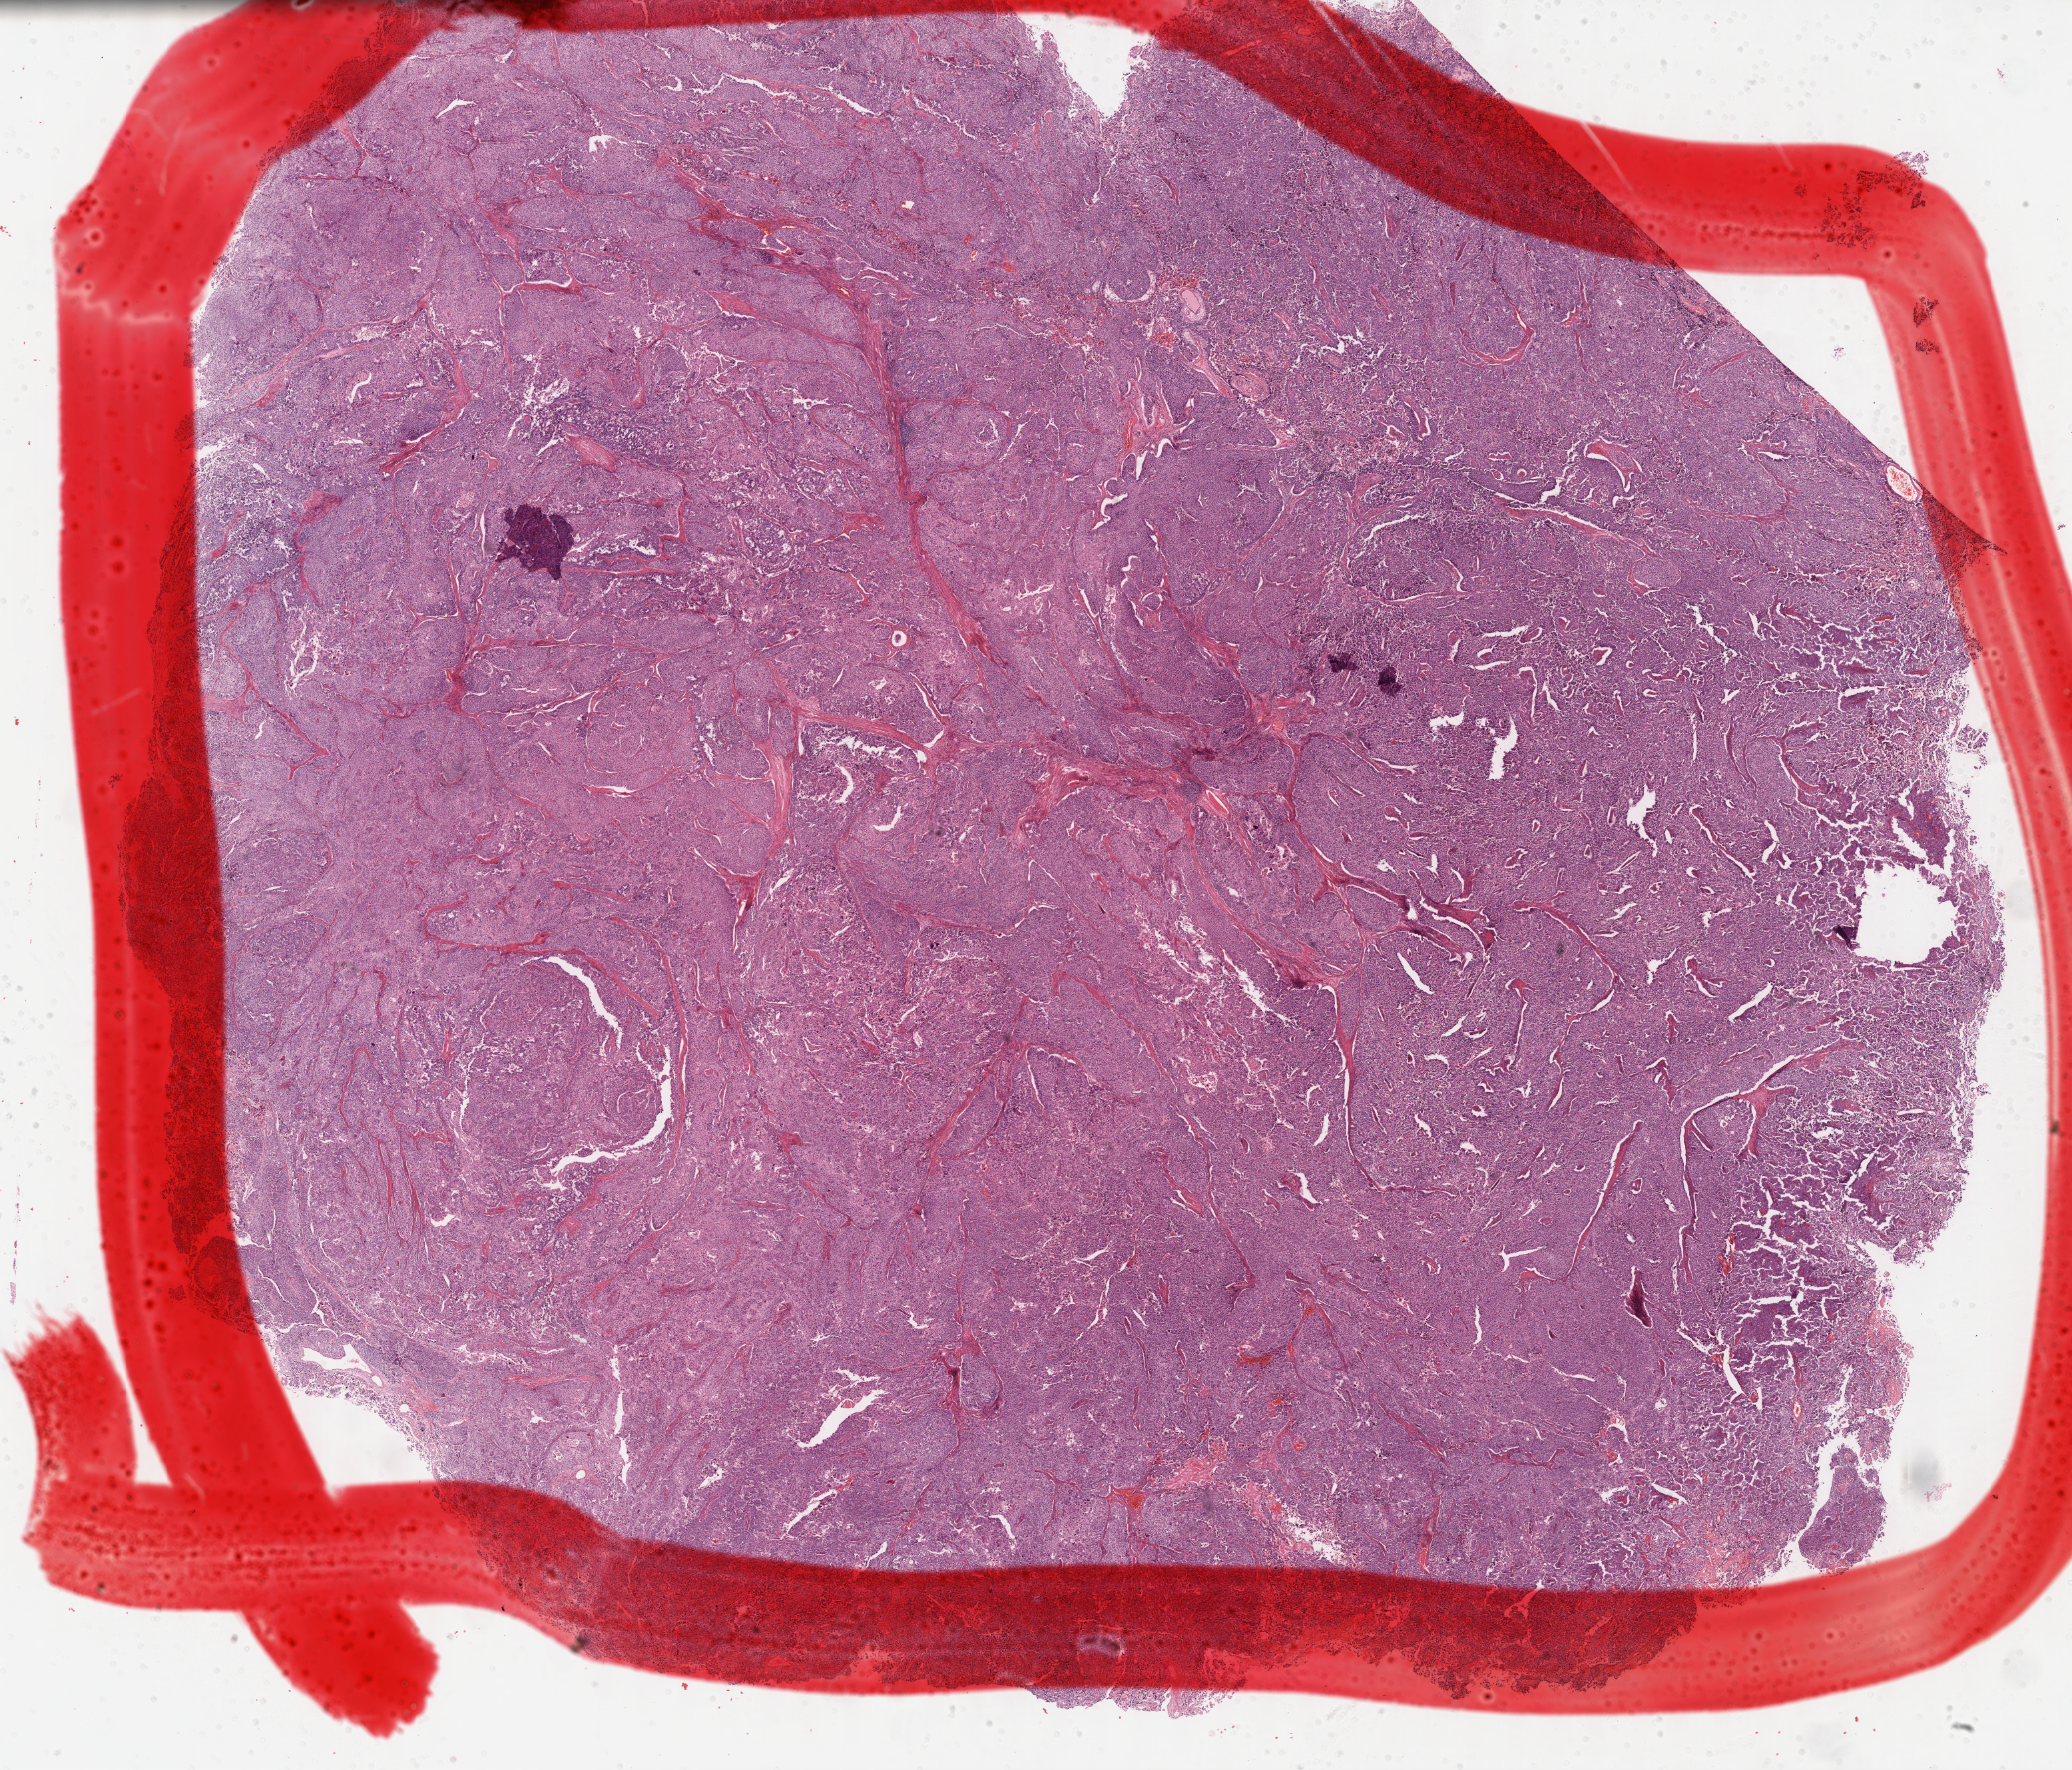
H&E-stained whole-slide image — shown as a low-resolution overview of the whole scanned area (about 25.2 x 21.5 mm, slide scanned at 40x); formalin-fixed paraffin-embedded (FFPE) diagnostic section; sample: primary tumour, bladder. Patient: male, age at initial diagnosis 63 years. Histologic grade: high grade.
- AJCC pathologic stage: III (7th edition)
- pathologic diagnosis: Transitional cell carcinoma